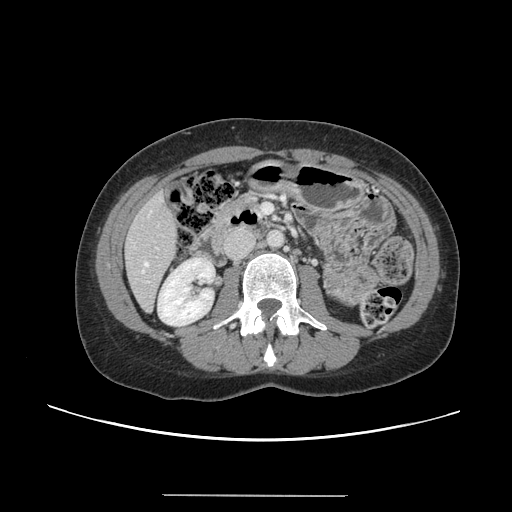
Contrast-enhanced abdominal CT, one axial slice; position 44 of 144 along the scan axis; 120 kVp; intravenous contrast given; soft-tissue window (W 400 / L 40 HU); 2.5 mm slice thickness; 512 × 512 image matrix. Female patient, age 53 years. Case-level facts recorded for this patient, not image findings: diagnosis: colorectal cancer liver metastases, imaged before liver resection; multiple liver metastases: yes; largest metastasis: 1.1 cm; chemotherapy before resection: no.
Structures marked on this image (manually delineated by an expert):
- hepatic veins: box from (x=142, y=262) to (x=148, y=272) px
- liver: (x=125, y=195)–(x=179, y=310)
- planned liver remnant (the part of the liver to remain after resection): (x=126, y=195)–(x=179, y=310)
- portal vein (with intrahepatic branches): (x=147, y=248)–(x=158, y=283)